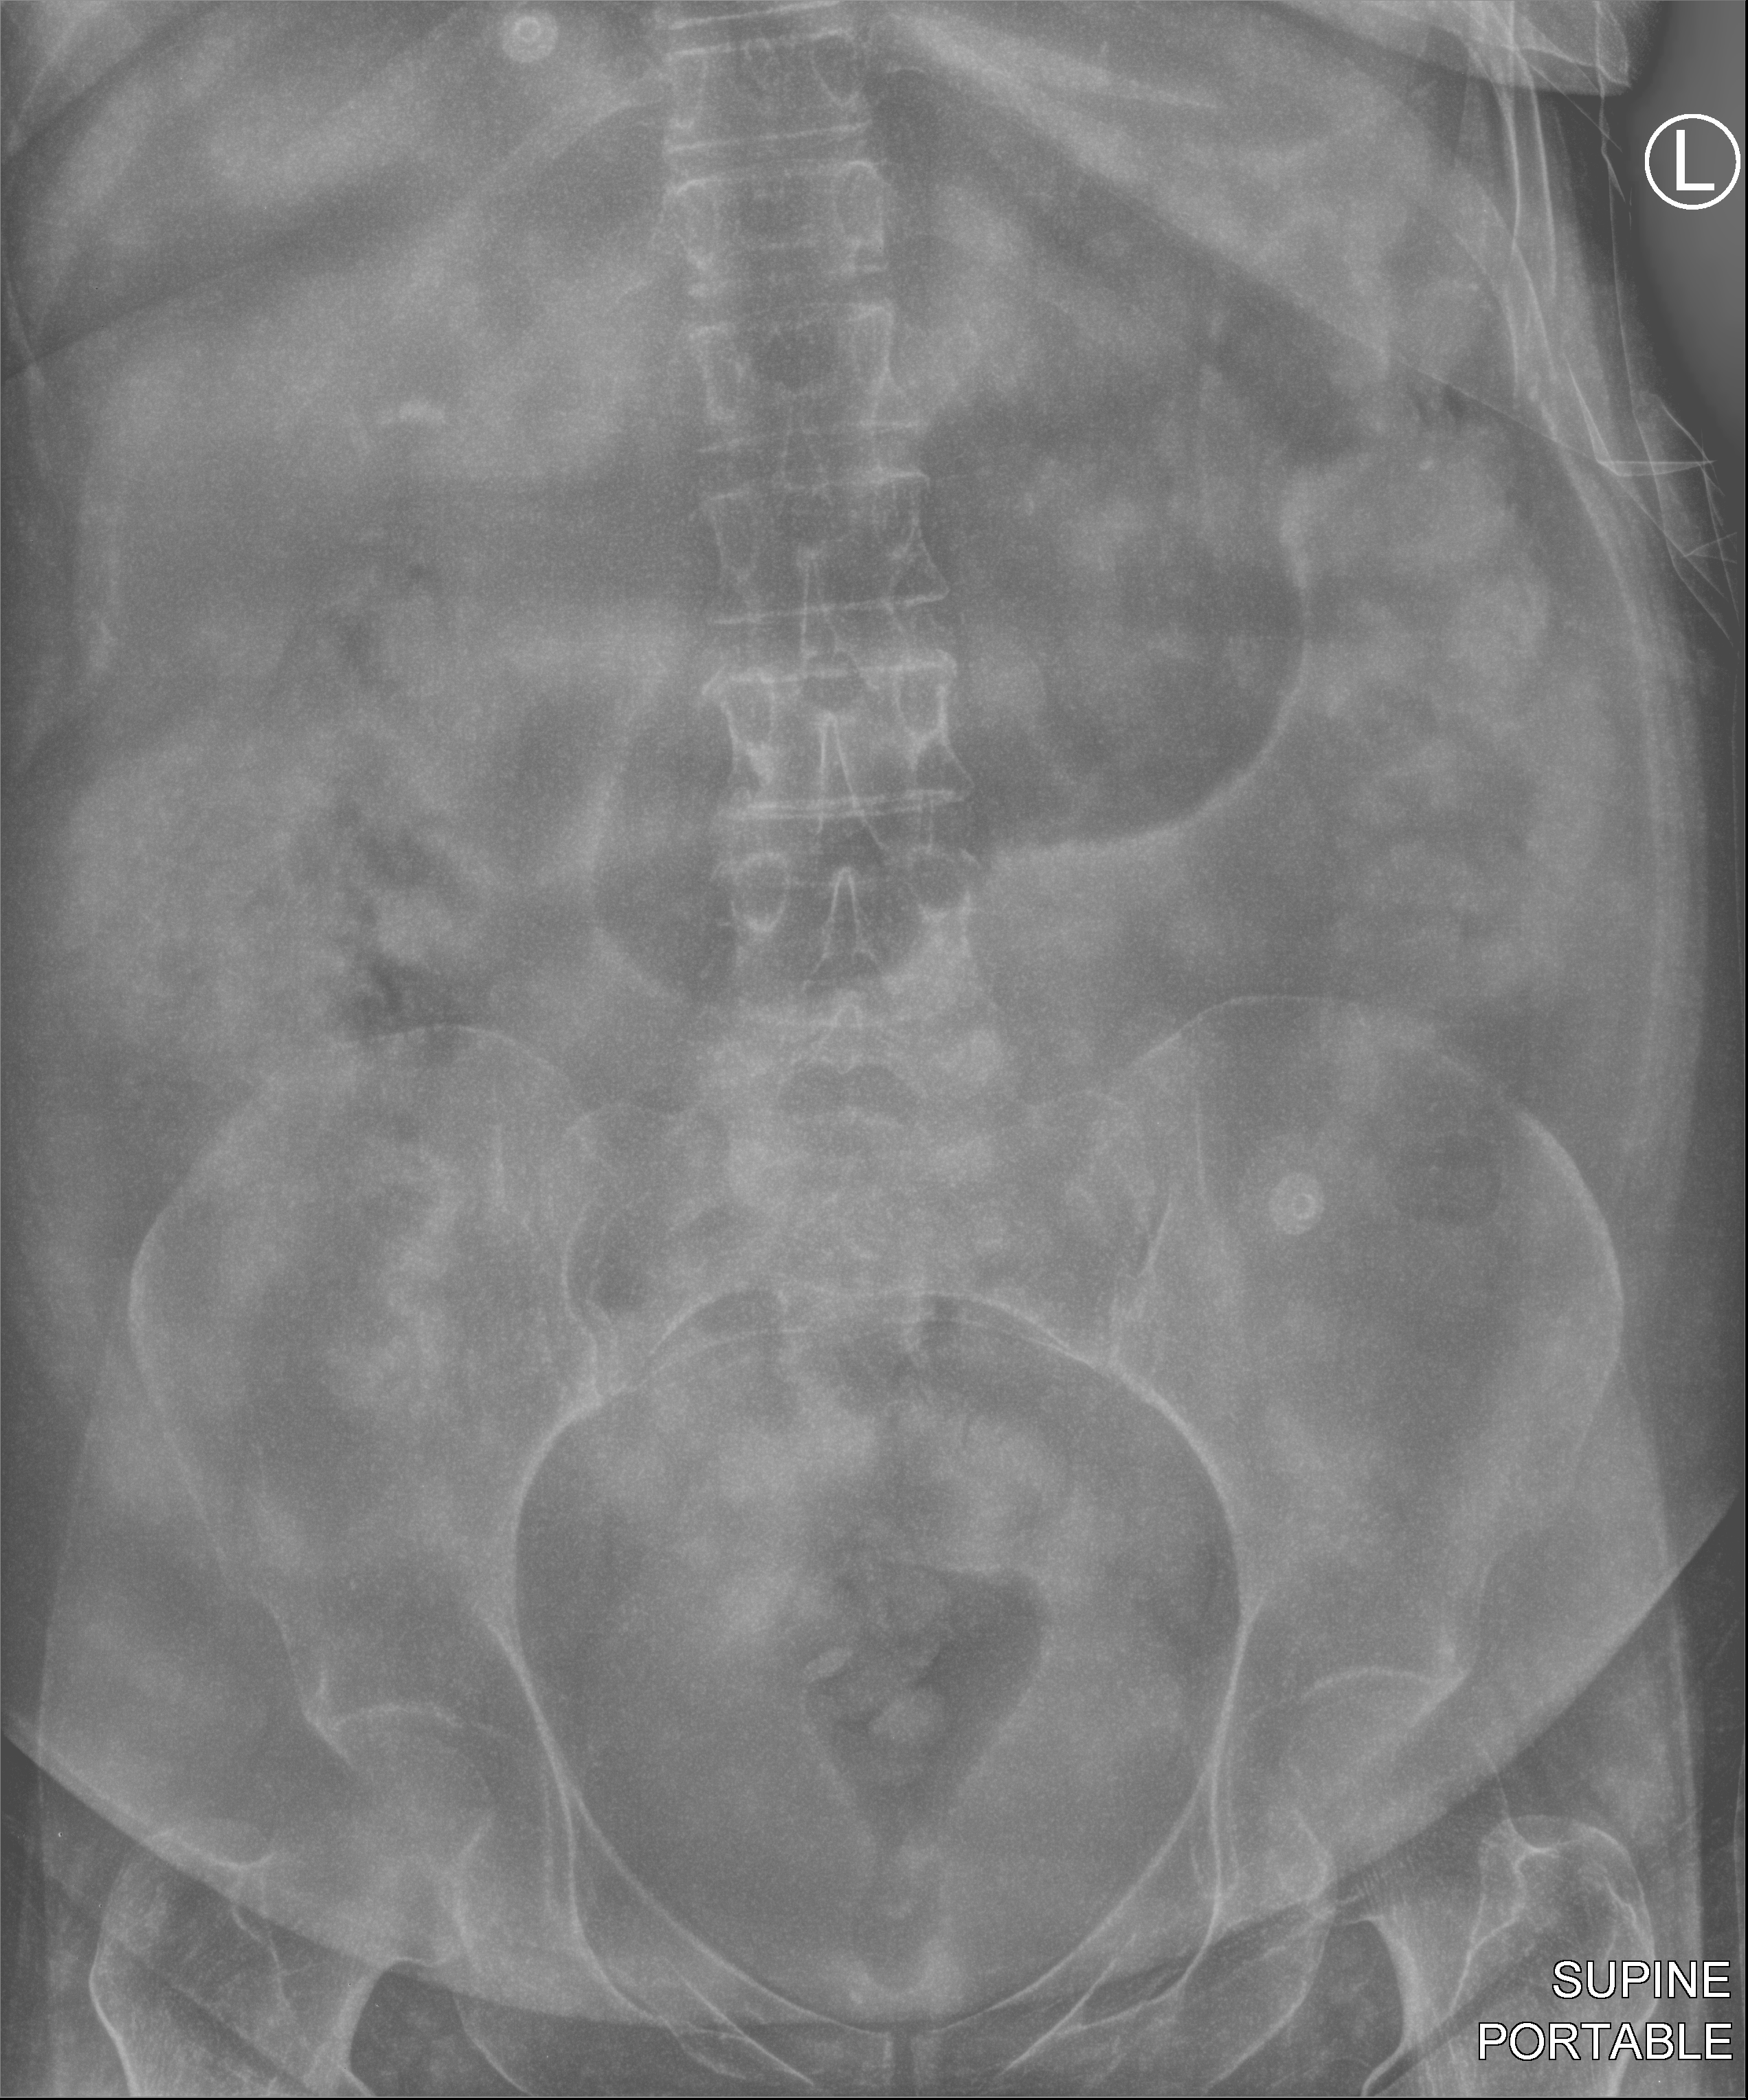
Bedside abdomen radiograph (computed radiography); anteroposterior (AP) projection. Patient hospitalised with COVID-19; female, aged 18–59 years.
Hospital-stay facts (about this admission, not read from this image; timing relative to this image not recorded): mechanically ventilated during this hospital stay: no; admitted to intensive care during this hospital stay: yes; length of hospital stay: 44 days.